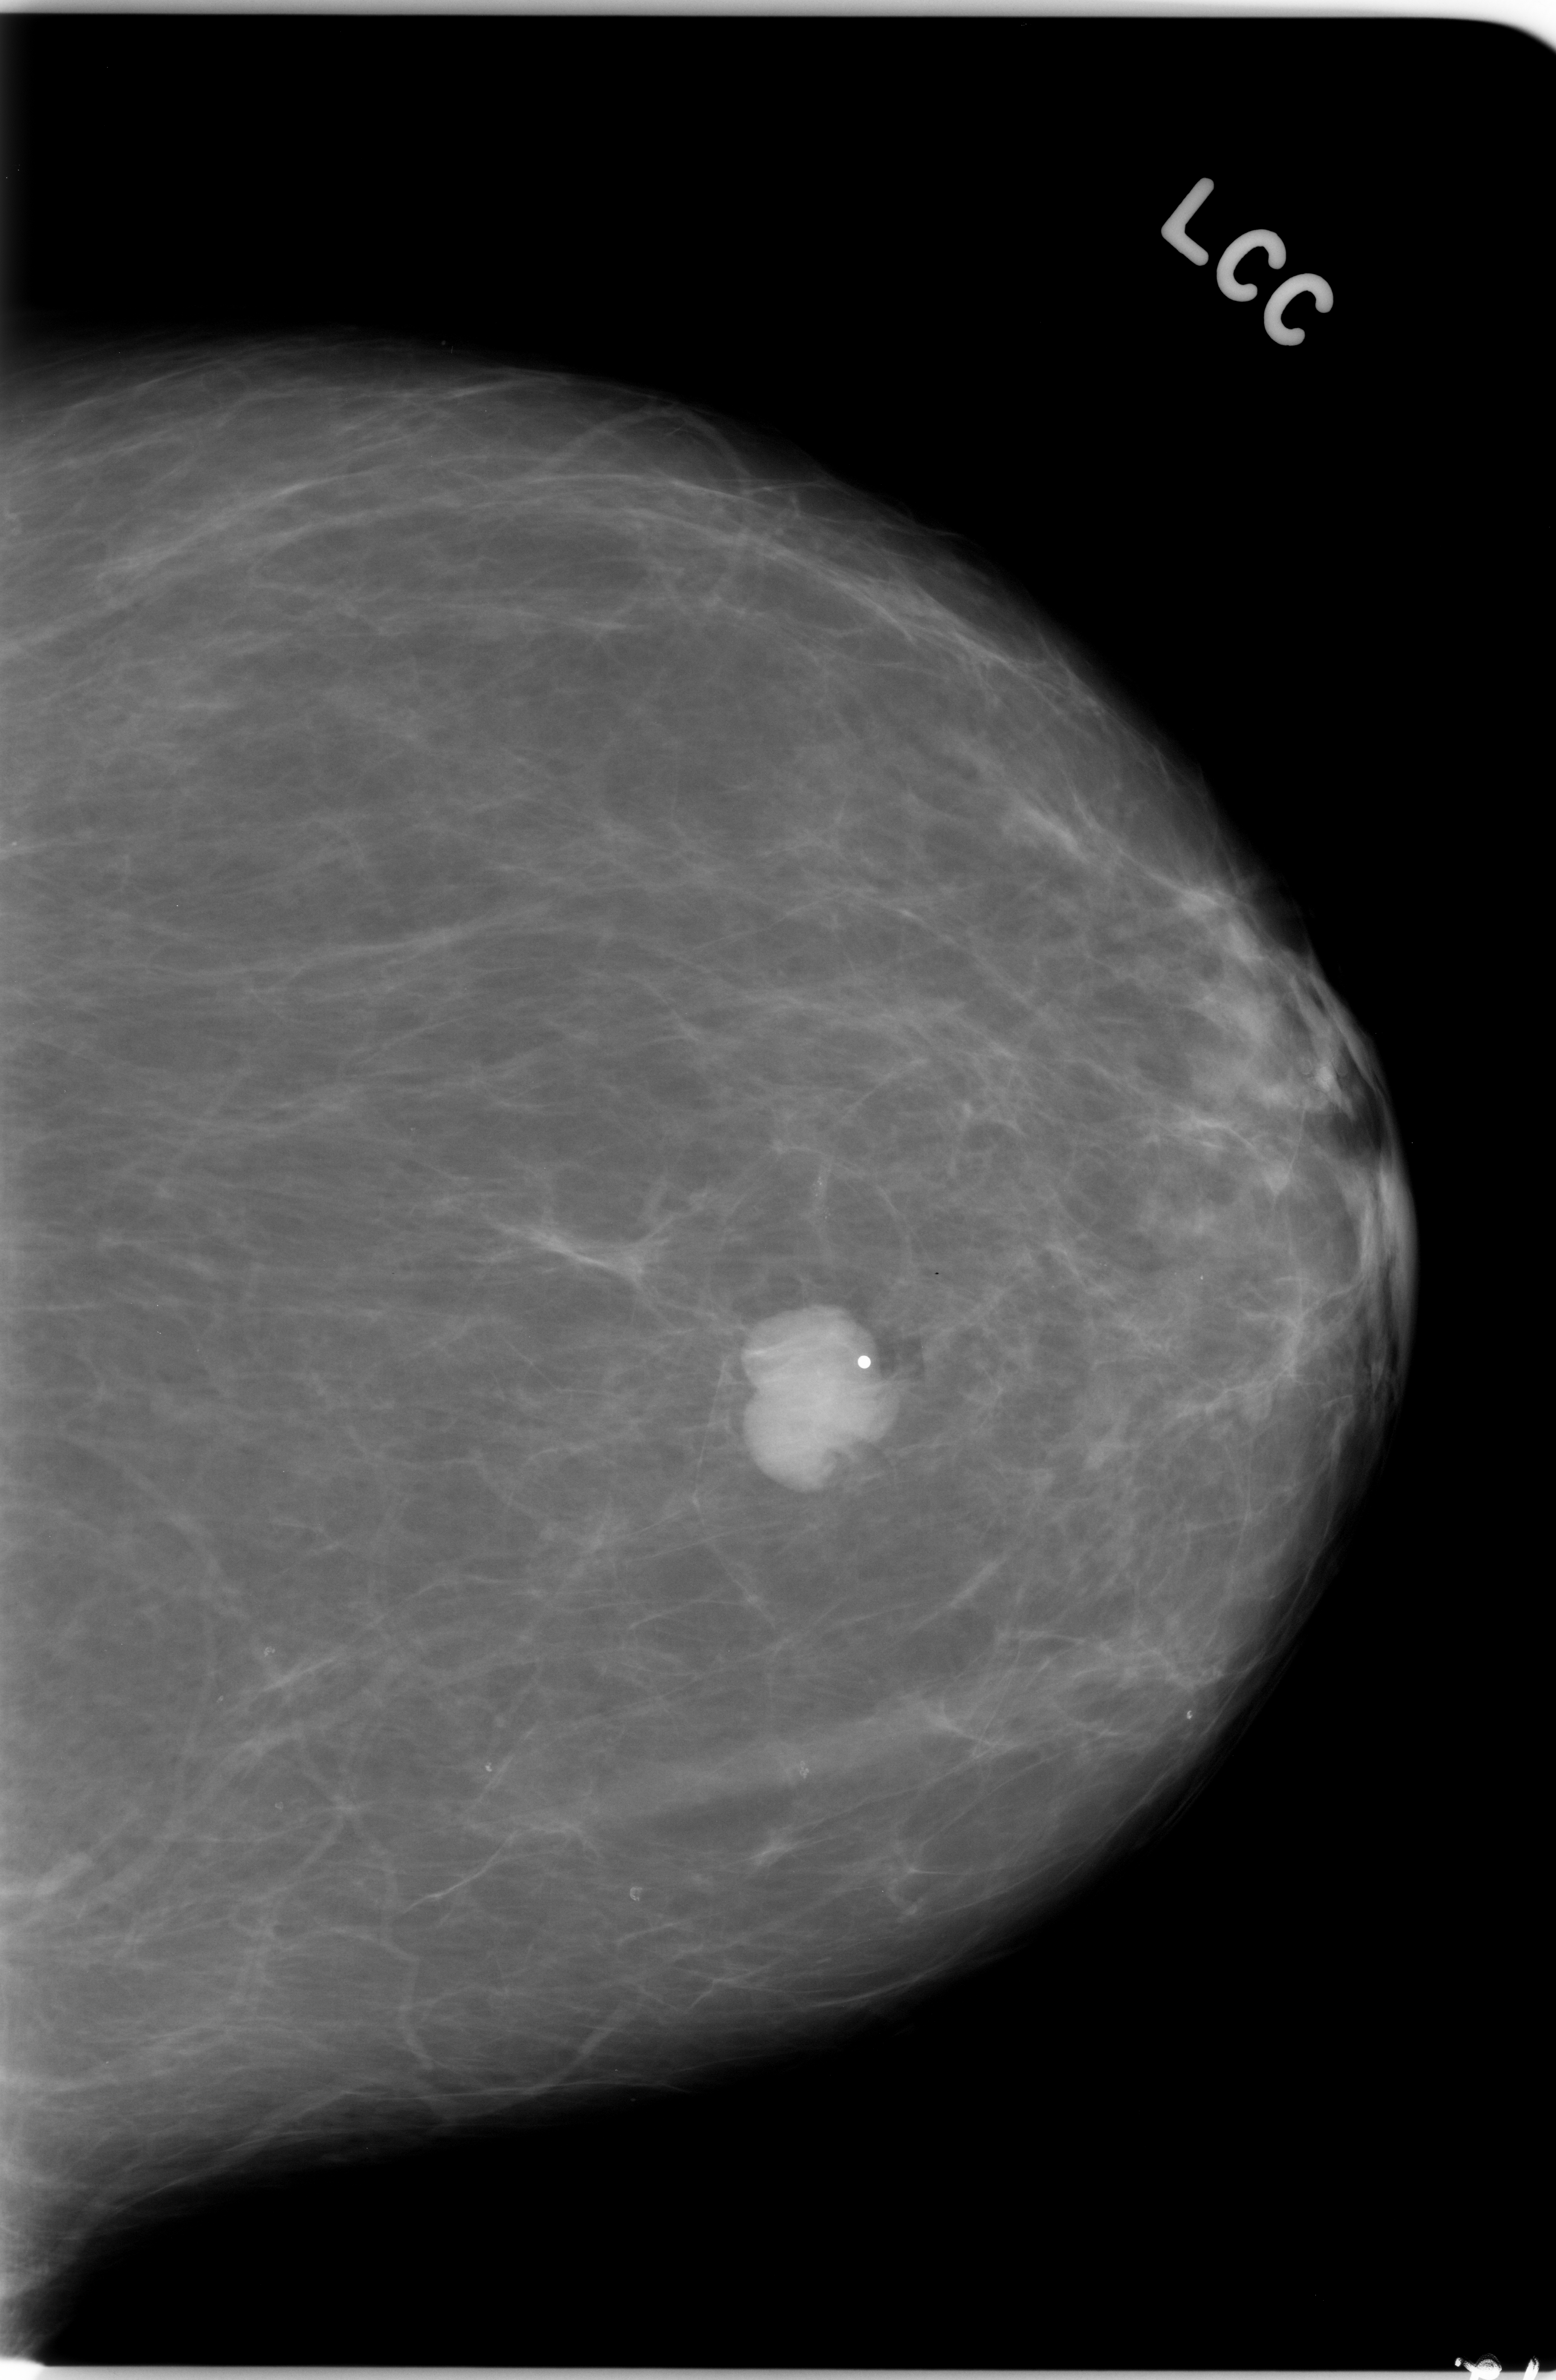
Mammogram (digitized film). Left breast. Craniocaudal (CC) view. 1556 × 2380 image matrix.
Marked abnormalities (boxes around the expert regions of interest):
- mass, shape lobulated, margins circumscribed; BI-RADS assessment category 5; pathology result (as recorded, not read from the image): malignant: box from (x=727, y=1338) to (x=895, y=1495) px